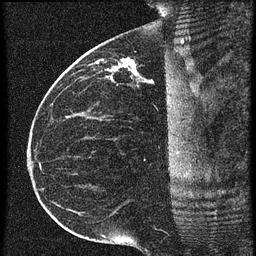
Breast MRI (dynamic contrast-enhanced), one sagittal slice; position 34 of 60 along the scan axis; 3 images stored at this slice position (order not interpretable as contrast timing); 1.5 T; TE 4.2 ms, TR 20.4 ms; 256 × 256 image matrix. Female patient, age 35 years. From the clinical record (not read from this slice): setting: breast cancer imaged before/during neoadjuvant chemotherapy; receptor status: HR-positive, HER2-negative.
Structures marked on this image (semi-automatically segmented with operator editing):
- analysis volume of interest (the breast-tissue region the enhancement analysis was run in; not a lesion): bounding box (x1, y1, x2, y2) in pixels: (84, 50, 179, 97)
- tumour enhancement mask (voxels above the 90 % enhancement threshold inside the analysis volume of interest): (98, 60, 137, 73)